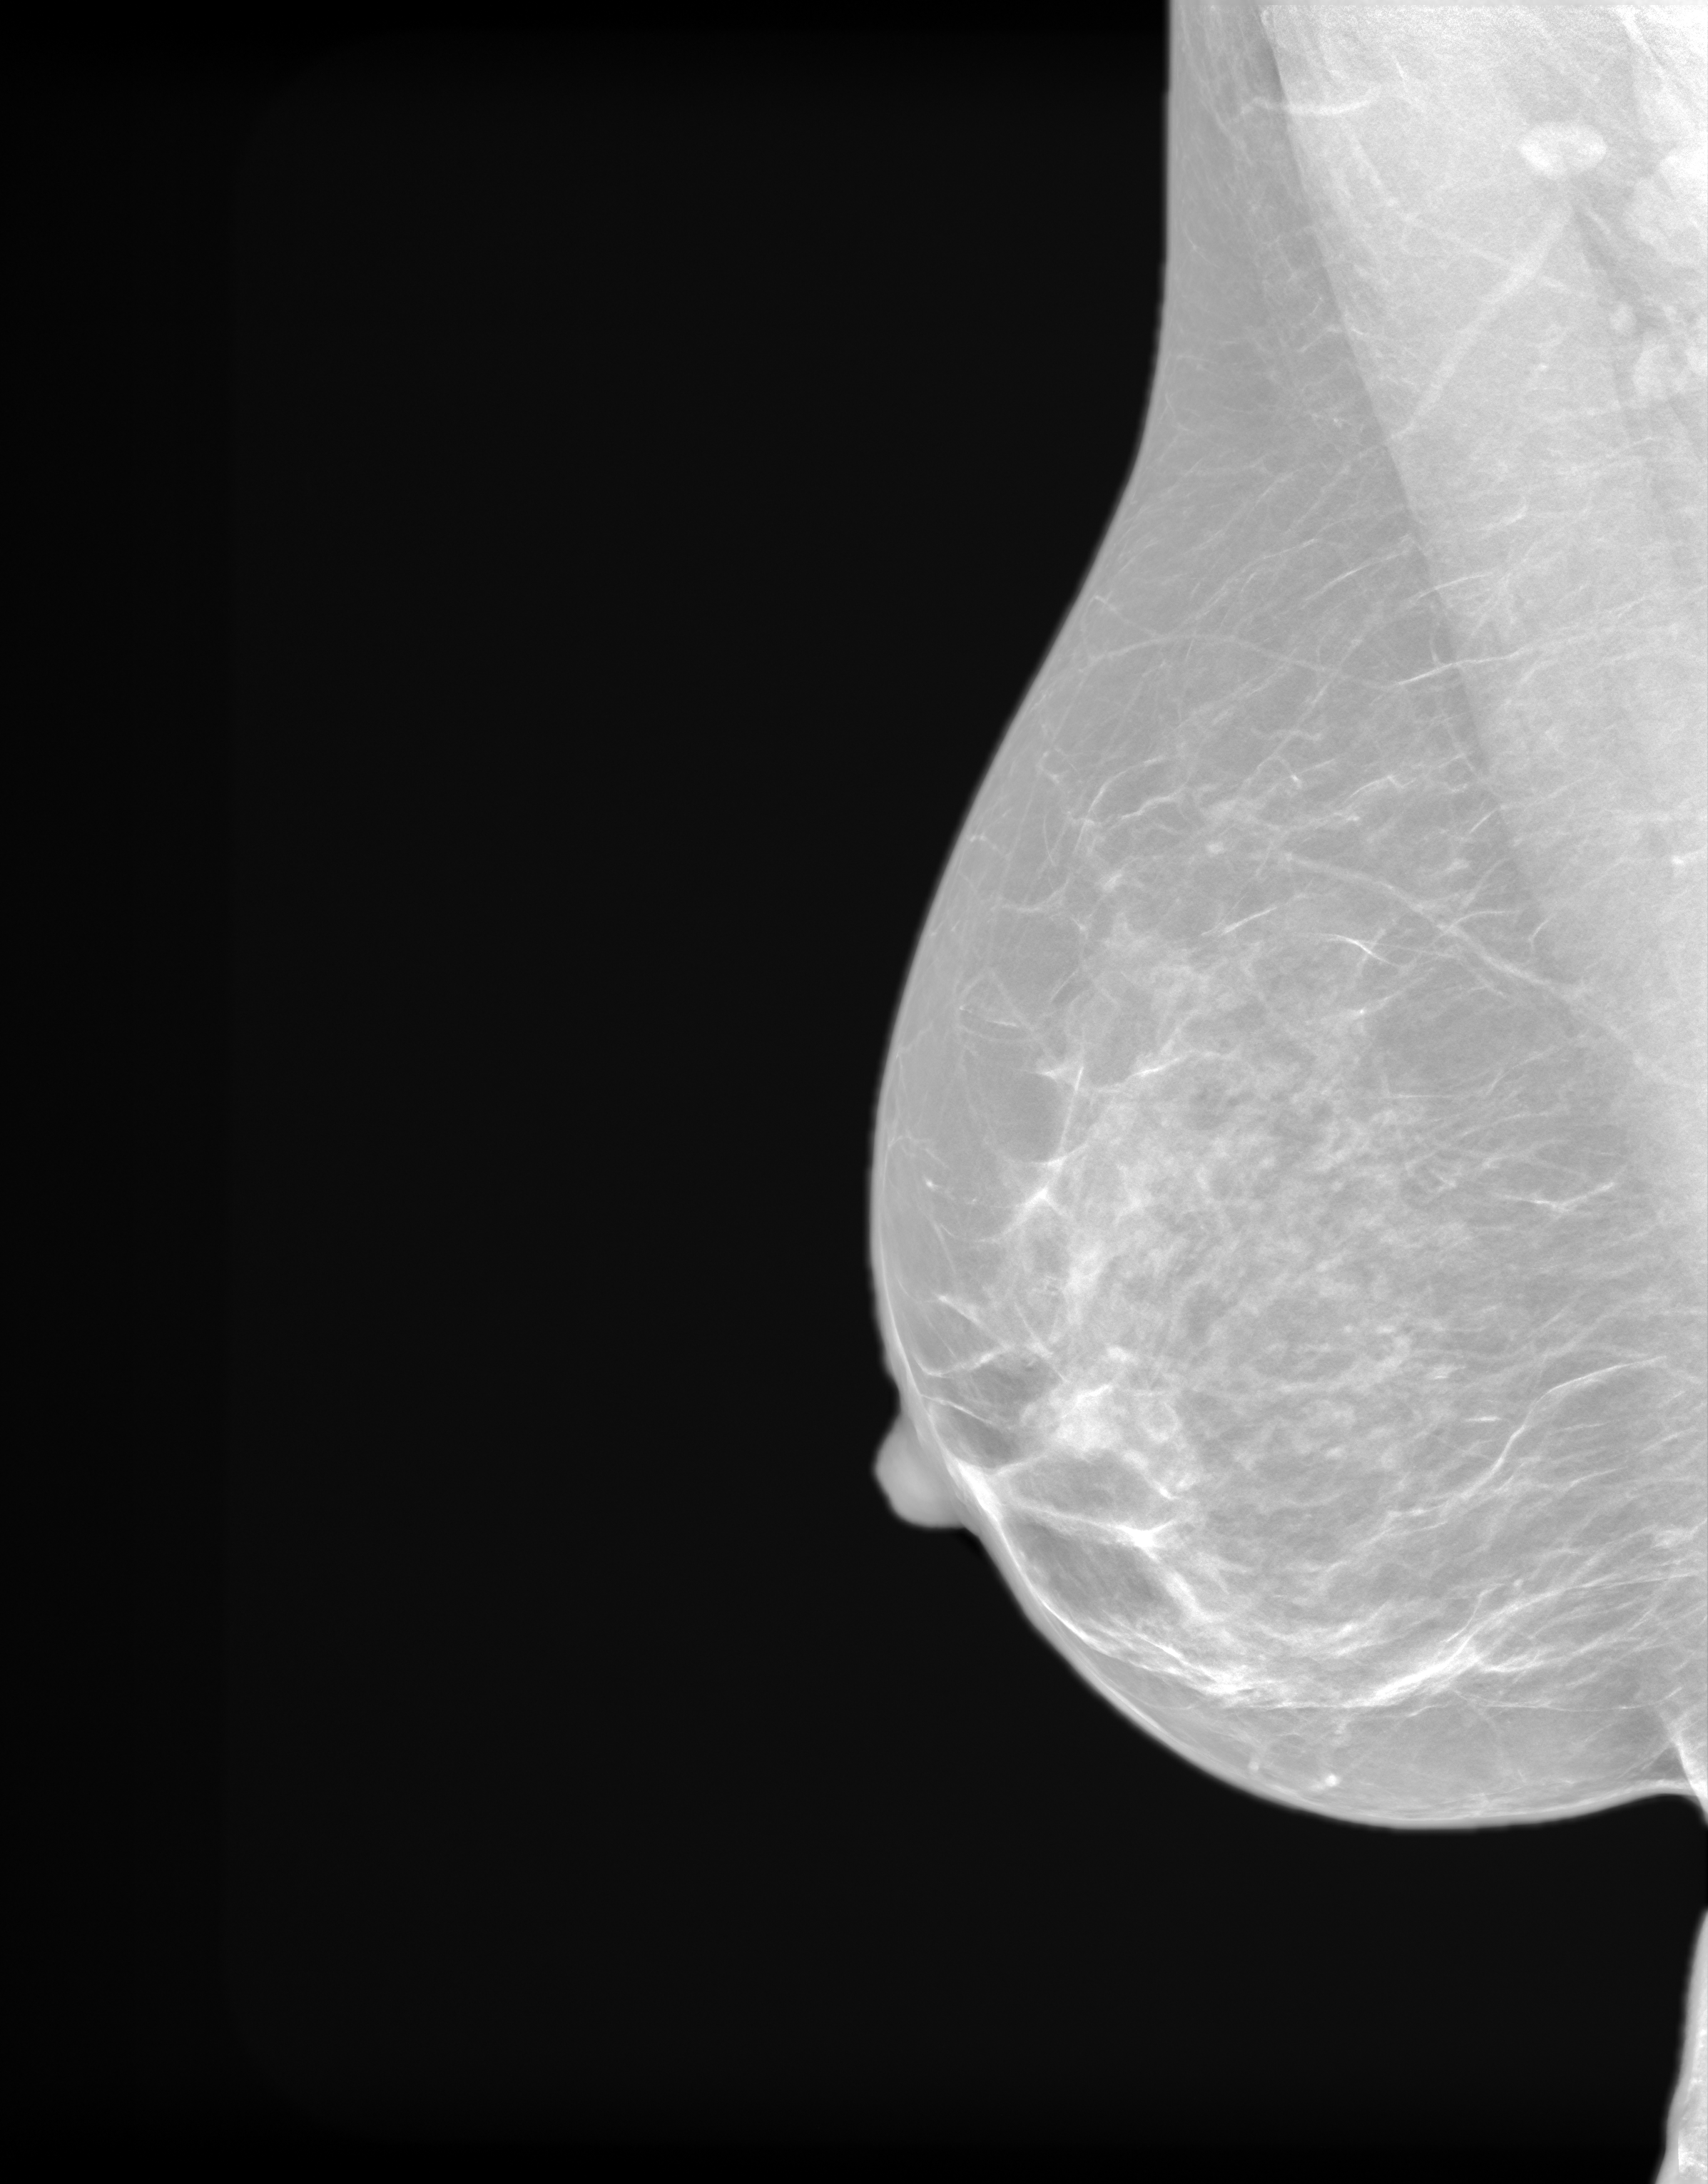
Screening examination. Patient aged 54 years (female).
Image type: synthesized 2-D view from tomosynthesis. Breast: right. Projection: medio-lateral oblique projection.